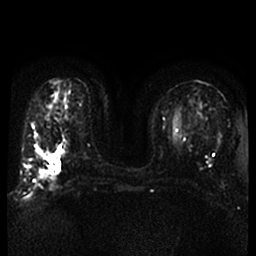
Breast MRI, one axial slice; position 17 of 52 along the scan axis; diffusion-weighted series; image 2 of 4 stored at this slice position (different b-values; order by instance number); 1.5 T; 256 × 256 image matrix, field of view 320 × 320 mm. Female patient.
Structures marked on this image (outlined manually by an expert reader):
- tumour on diffusion-weighted imaging: box from (x=42, y=154) to (x=52, y=161) px